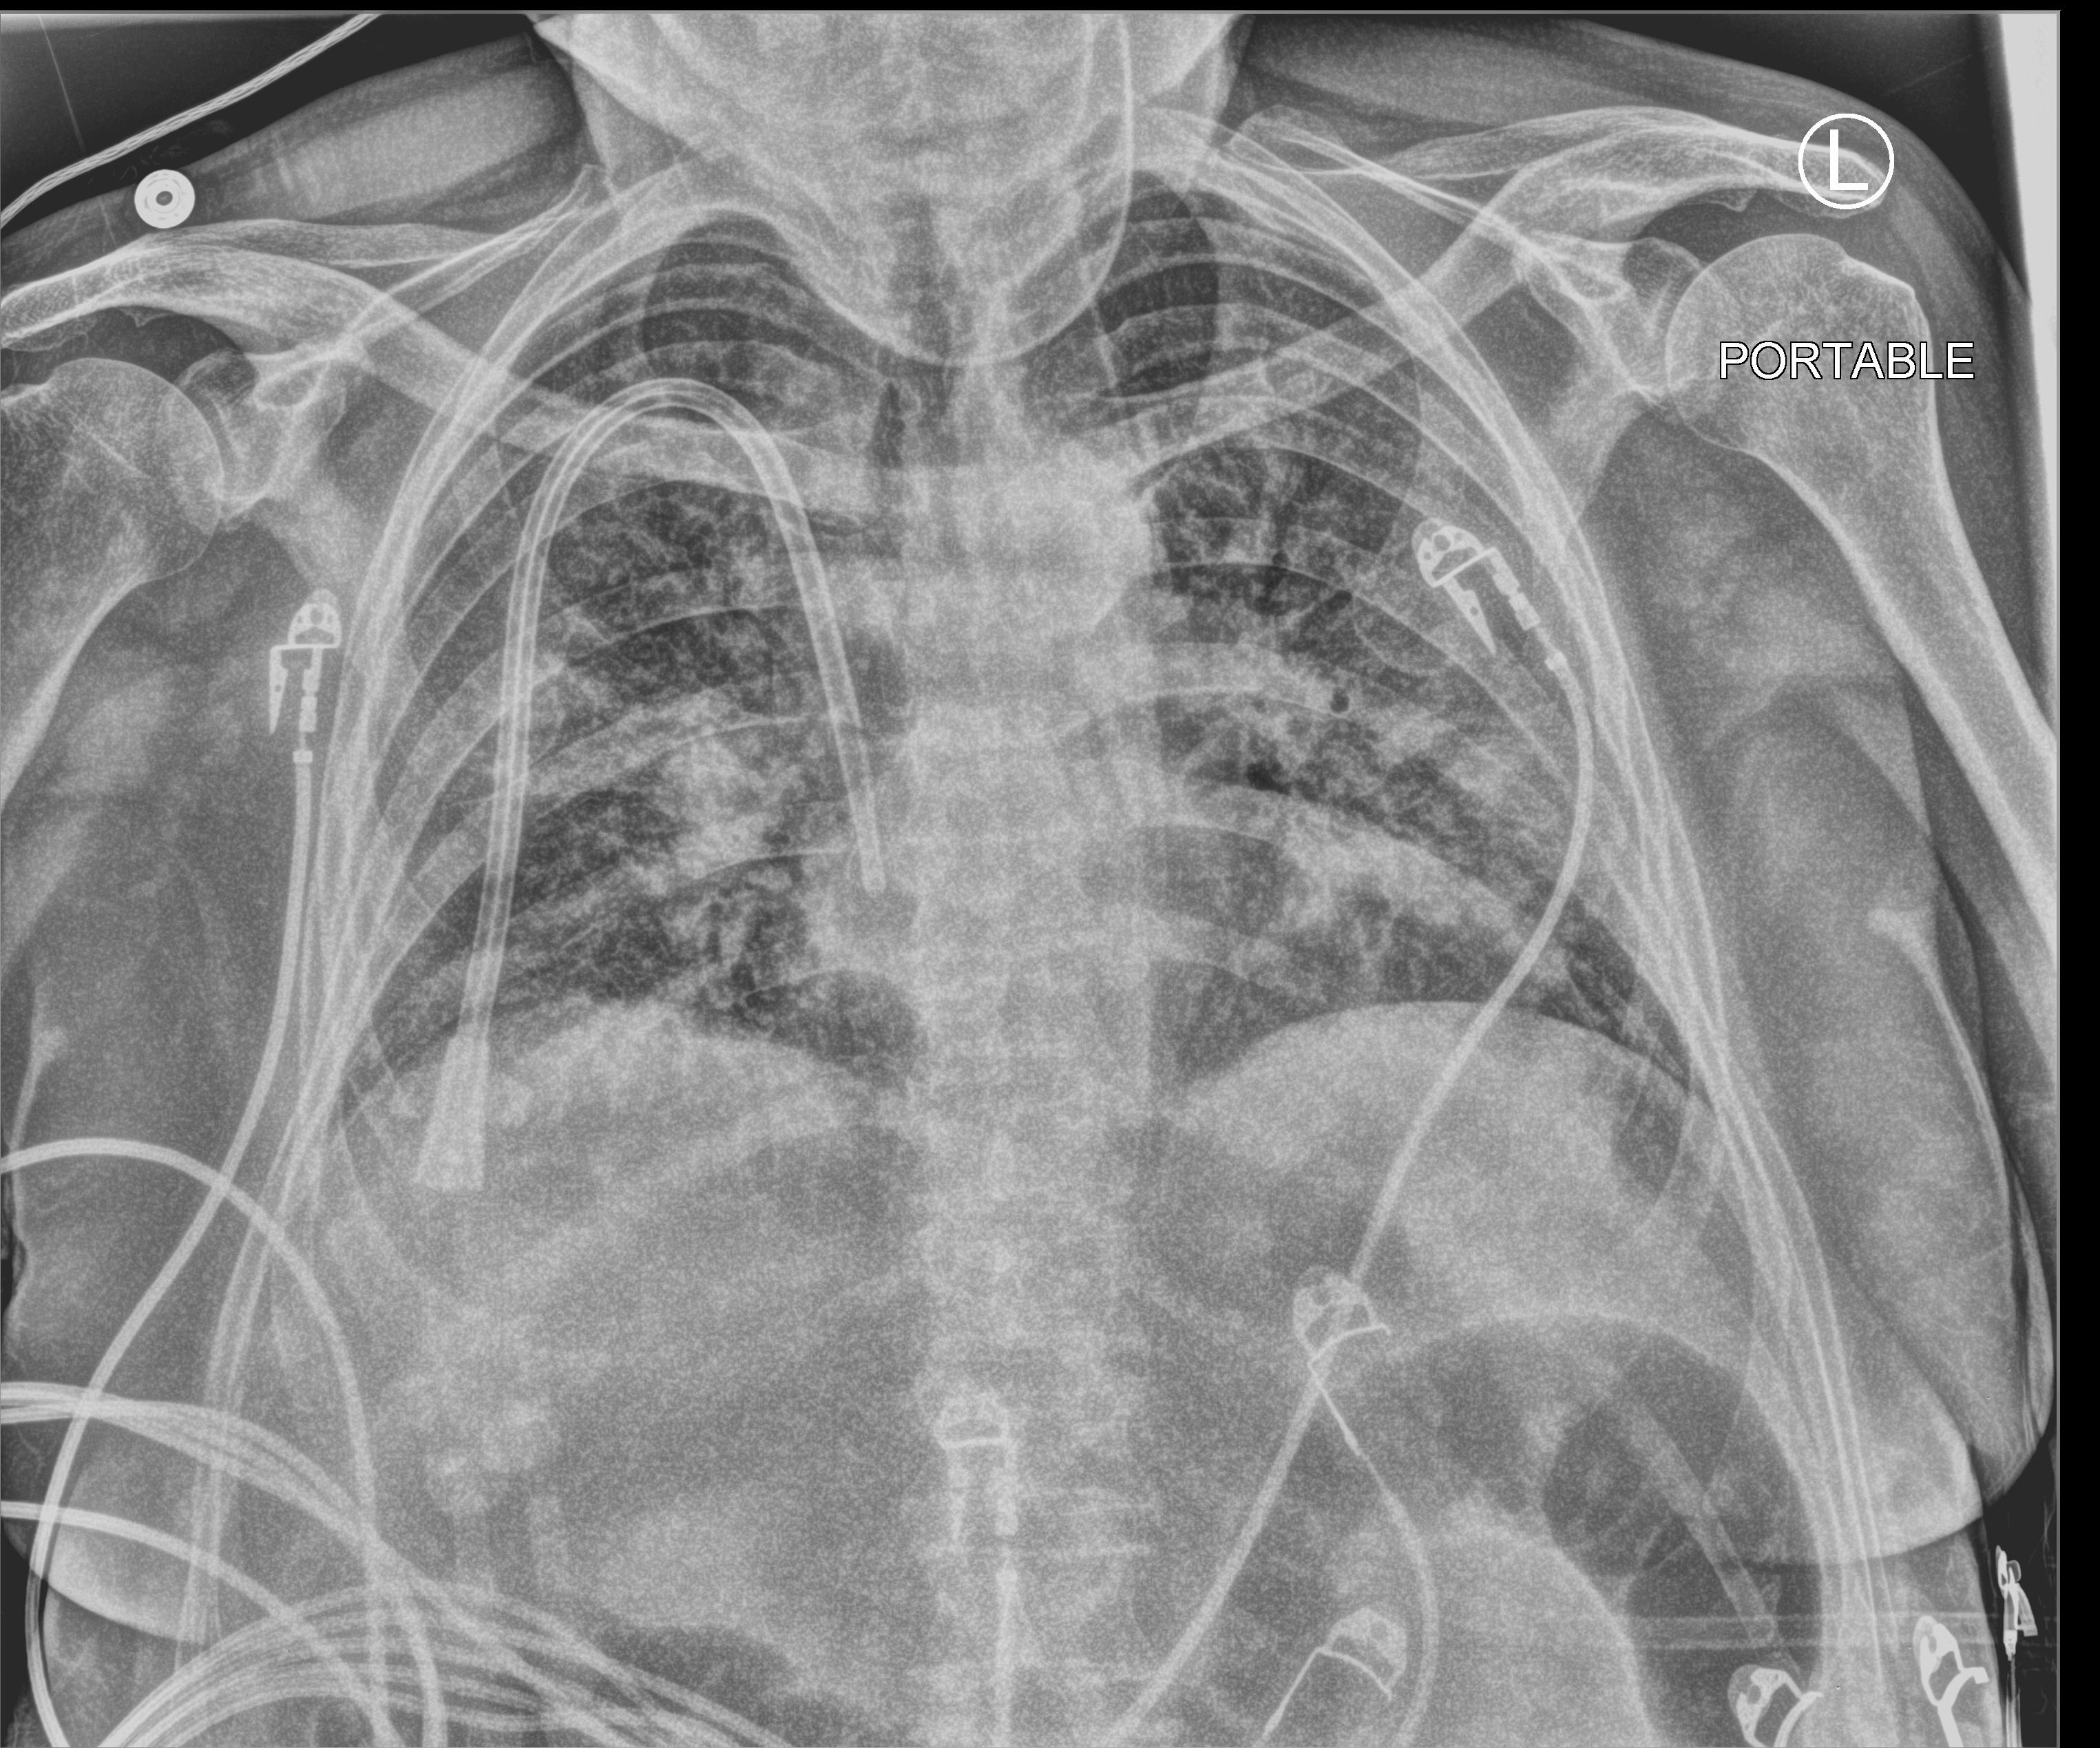
Portable chest radiograph; anteroposterior (AP) projection. Male patient hospitalised with COVID-19, age 60–74 years.
From the hospital-stay record, not from the radiograph (when in the stay this image was taken is not recorded): mechanically ventilated during this hospital stay: no.